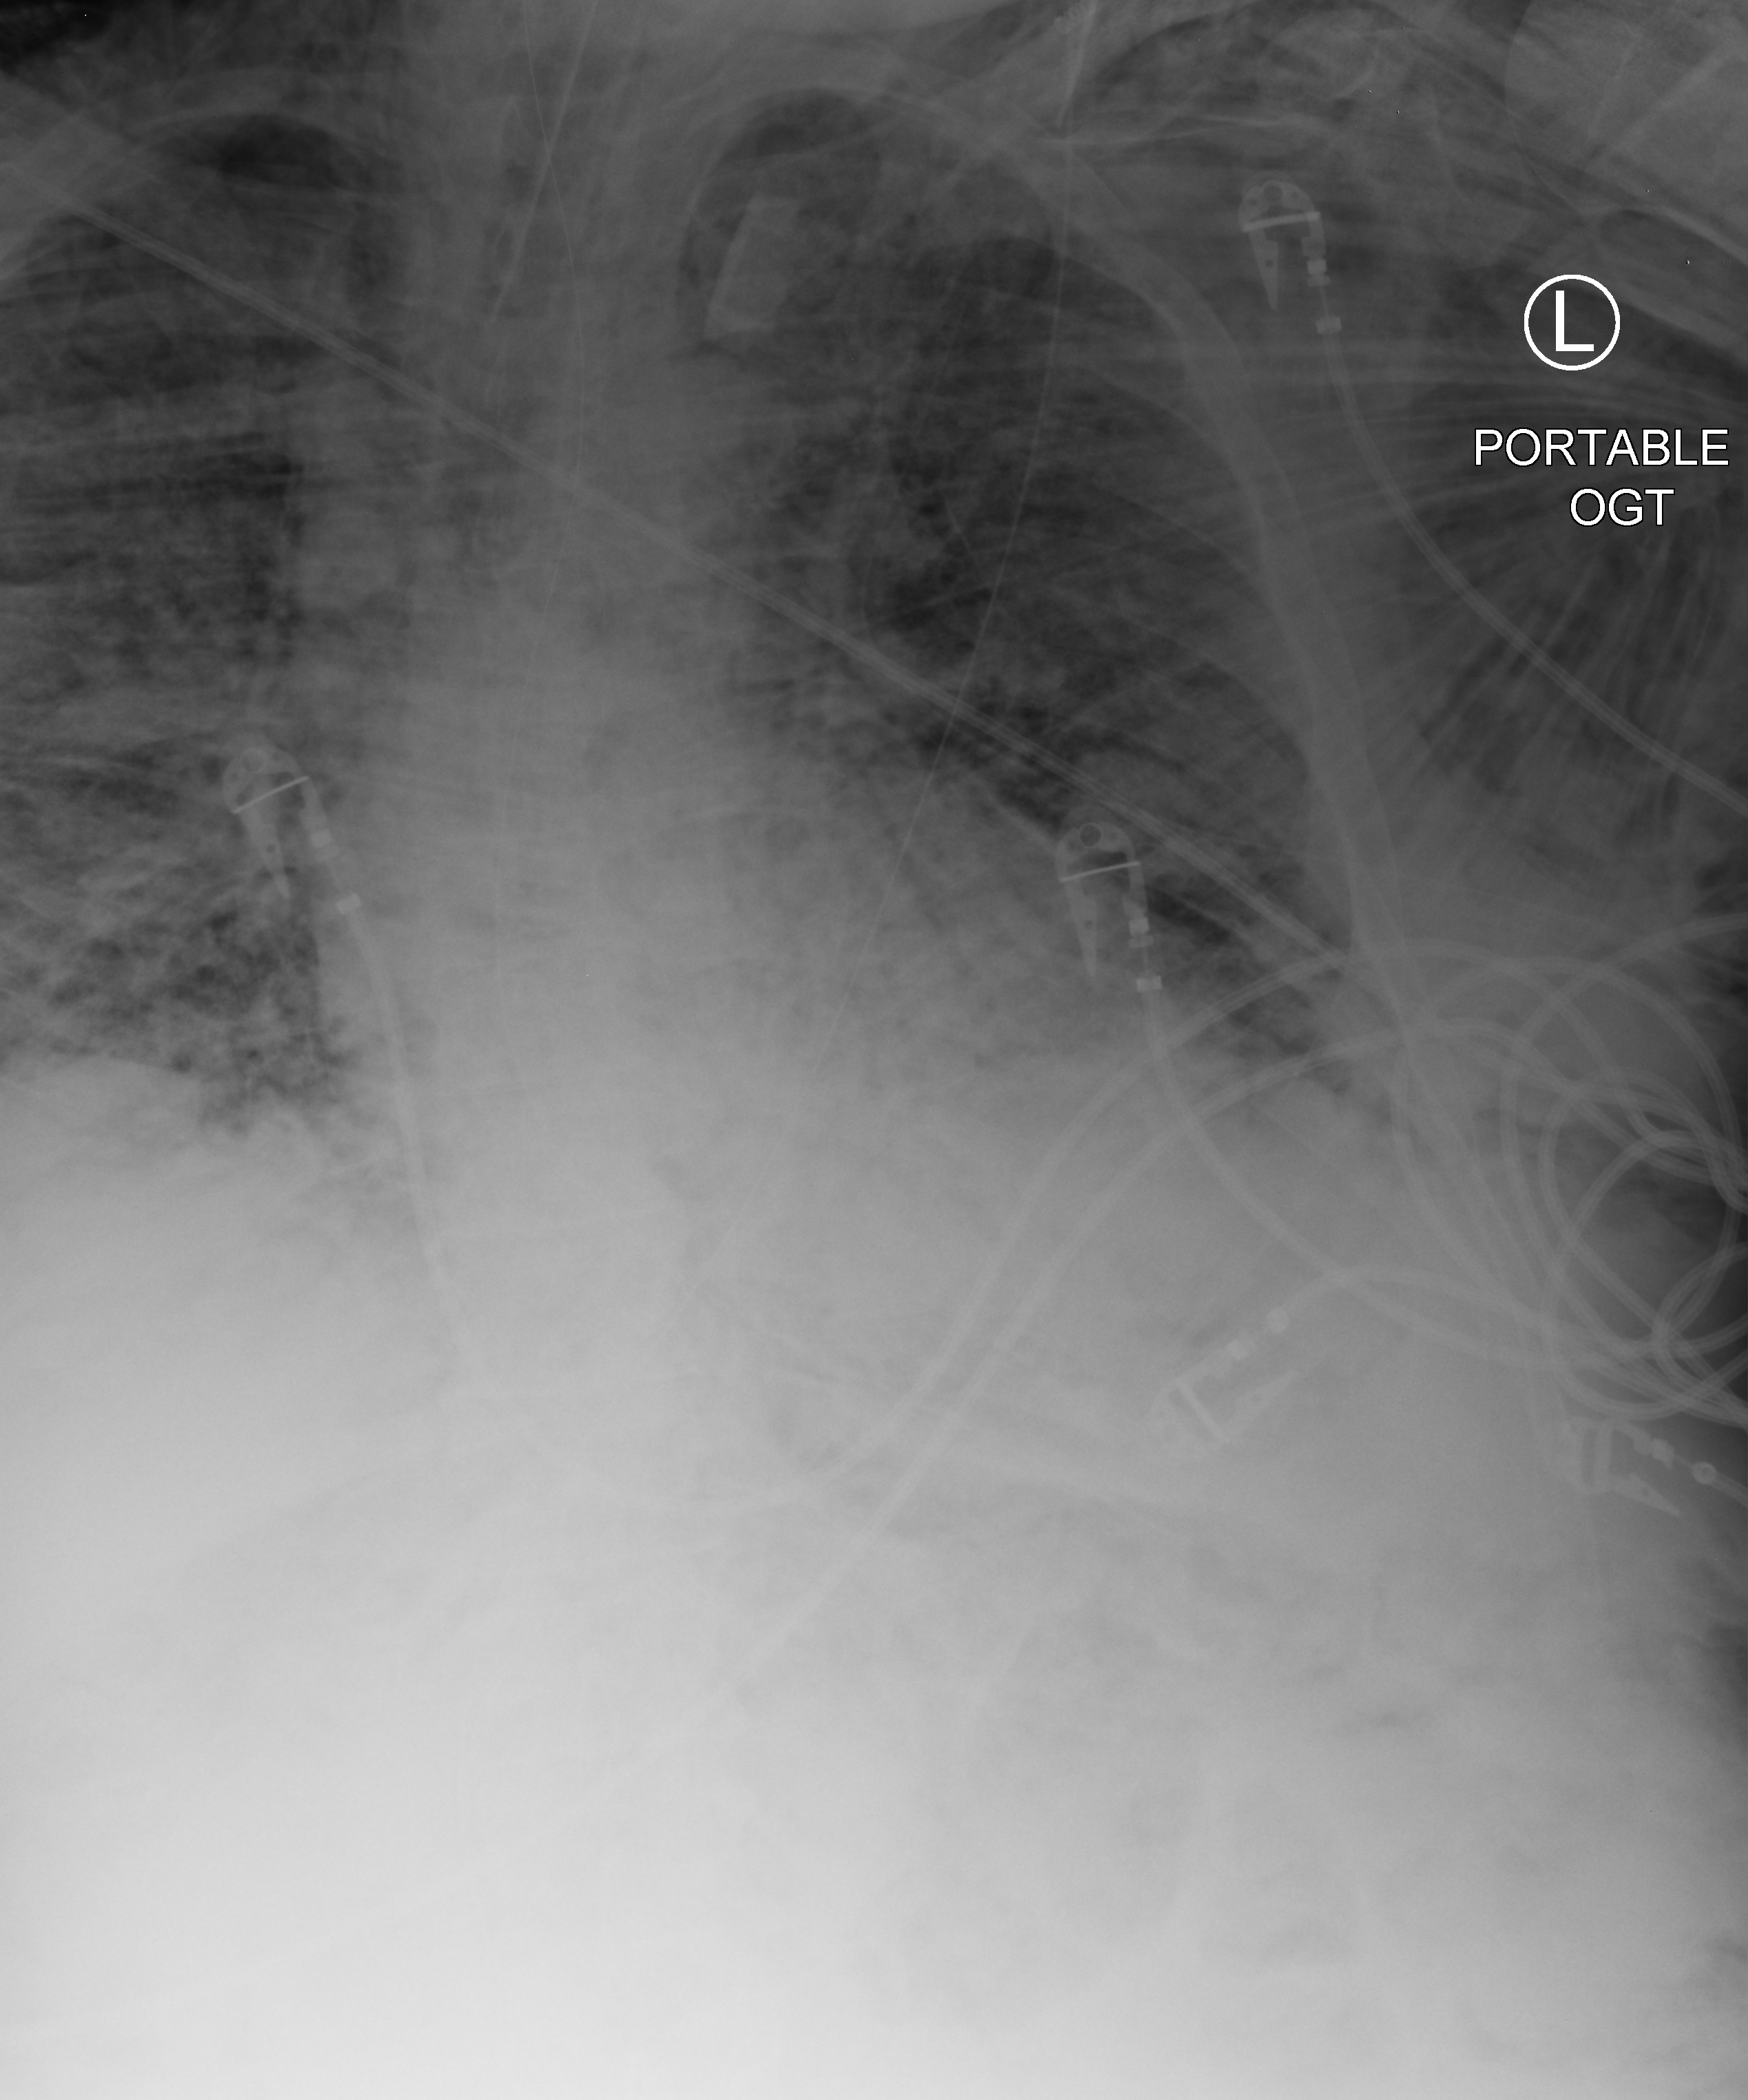
Chest X-ray (portable), anteroposterior (AP) projection. Patient hospitalised with COVID-19, aged 18–59 years.
Hospital-stay facts (about this admission, not read from this image; timing relative to this image not recorded): mechanically ventilated during this hospital stay: yes.